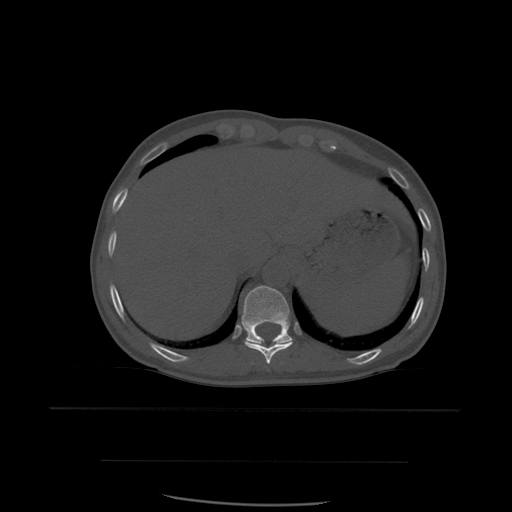
CT including the spine, one axial slice; bone window (W 1800 / L 400 HU); 1.25 mm slice thickness; 512 × 512 image matrix, field of view 392 × 392 mm. Patient age 48 years. Case-level facts recorded for this patient, not image findings: primary cancer: lung; vertebrae with lytic lesions (as recorded): T11.
Outlined on this slice (semi-automatically segmented with operator editing):
- T10 vertebra: bounding box [x1, y1, x2, y2] px = [244, 341, 293, 364]
- T11 vertebra: [242, 286, 293, 346]